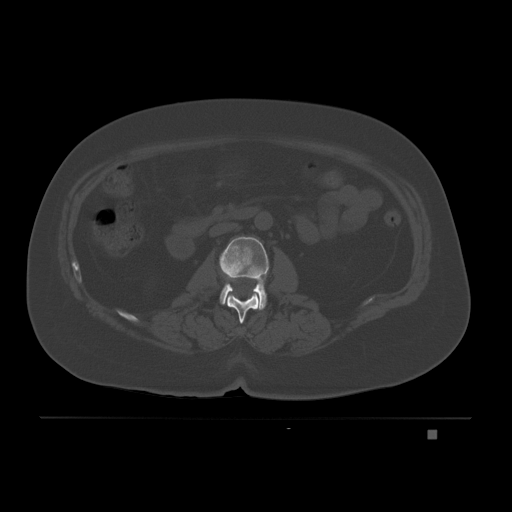
CT including the spine, one axial slice. Slice 66 of 221 in the series (ordered by position). Bone window (W 1800 / L 400 HU). 3 mm slice thickness. 512 × 512 image matrix, field of view 474 × 474 mm. Patient: female, 63 years. From the clinical record (not read from this slice): primary cancer: breast.
Outlined on this slice (semi-automatic segmentation, software-assisted and operator-edited):
- L1 vertebra: bounding box <219,261,263,324> (left, top, right, bottom; pixels)
- L2 vertebra: <219,236,270,310>